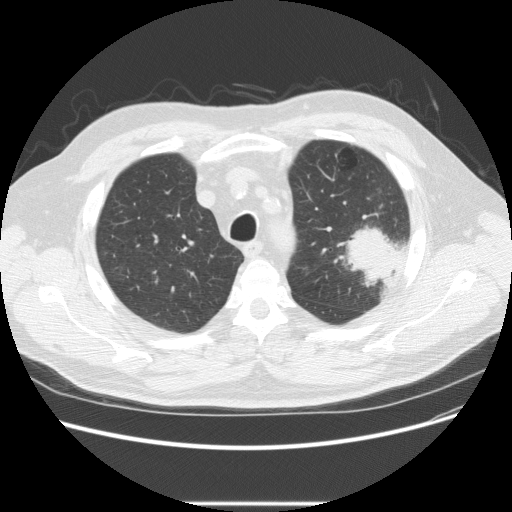
Low-dose screening chest CT, one axial slice. Lung window (W 1500 / L -600 HU). 512 × 512 image matrix.
Outlined on this slice (outlined manually by an expert reader):
- lesion 1 (tumor, upper lobe of left lung): bounding box [x1, y1, x2, y2] px = [345, 226, 401, 288]